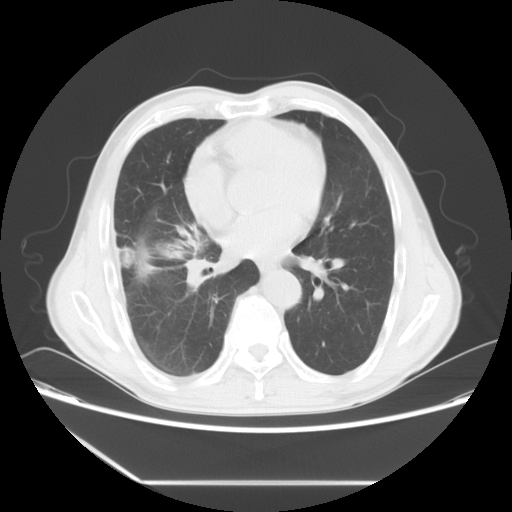
Chest CT, one axial slice. Position 27 of 60 along the scan axis. Reconstruction kernel STANDARD. 120 kVp. Lung window (W 1500 / L -600 HU). 5 mm slice thickness. 512 × 512 image matrix, field of view 386 × 386 mm. Patient: male, 72 years. Case-level facts recorded for this patient, not image findings: clinical TNM (as recorded): T1c N0 M0.
Structures marked on this image (rectangle marked by the reading radiologist):
- lung tumour (recorded histology: squamous cell carcinoma): bounding box <119,230,204,283> (left, top, right, bottom; pixels)